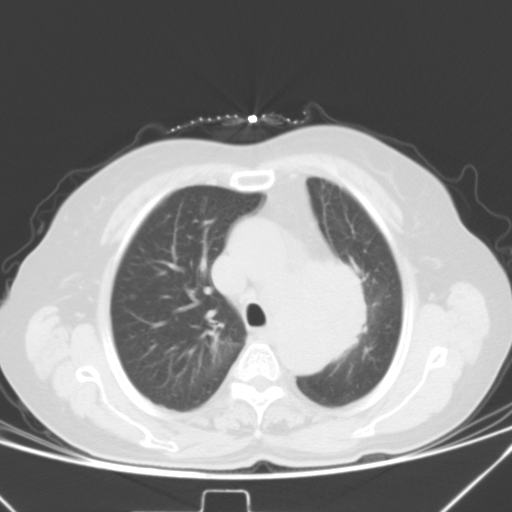
Chest CT, one axial slice; position 31 of 42 along the scan axis; lung window (W 1500 / L -600 HU); 5 mm slice thickness; 512 × 512 image matrix, field of view 331 × 331 mm. Patient: female, 59 years. From the clinical record (not read from this slice): clinical TNM (as recorded): T3 N1 M0.
Outlined on this slice (bounding box drawn by a radiologist):
- lung tumour (recorded histology: small cell carcinoma): bounding box (x1, y1, x2, y2) in pixels: (337, 253, 387, 367)